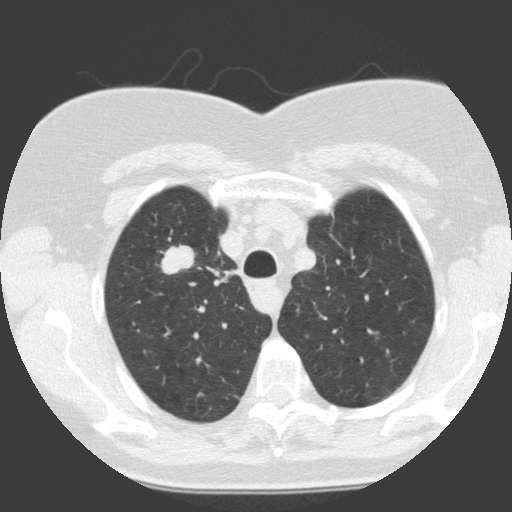
Low-dose screening chest CT, one axial slice; slice 116 of 146 in the series (ordered by position); 120 kVp; lung window (W 1500 / L -600 HU); 2 mm slice thickness; 512 × 512 image matrix, field of view 300 × 300 mm.
Structures marked on this image (expert manual segmentation):
- lesion 1 (tumor, upper lobe of right lung): bounding box [x1, y1, x2, y2] px = [160, 244, 195, 275]